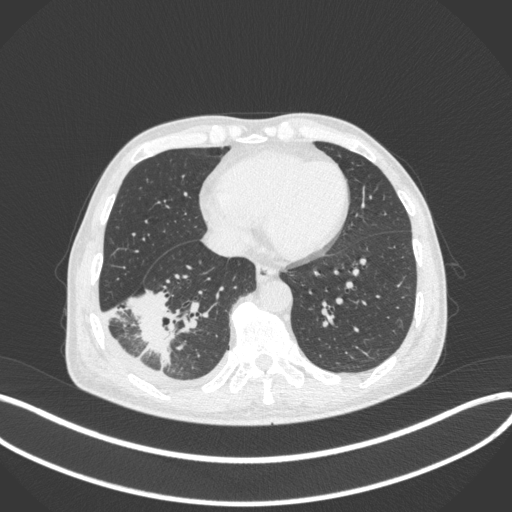
Chest CT, one axial slice; position 123 of 385 along the scan axis; reconstruction kernel B31f; lung window (W 1500 / L -600 HU); 1 mm slice thickness; 512 × 512 image matrix. Male patient, age 64 years. Case-level facts recorded for this patient, not image findings: clinical TNM (as recorded): T3 N0 M0; histopathological grade: G2-3.
Annotated regions visible in this slice (bounding box drawn by a radiologist):
- lung tumour (recorded histology: adenocarcinoma): bounding box (x1, y1, x2, y2) in pixels: (124, 282, 176, 372)